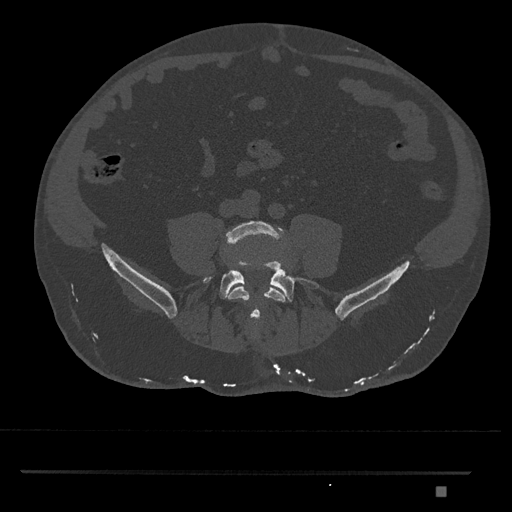
CT including the spine, one axial slice; slice 580 of 1134 in the series (ordered by position); 120 kVp; bone window (W 1800 / L 400 HU); 512 × 512 image matrix, field of view 429 × 429 mm. Patient: male, 65 years. Case-level facts recorded for this patient, not image findings: primary cancer: prostate.
Annotated regions visible in this slice (semi-automatically segmented with operator editing):
- L4 vertebra: box from (x=224, y=221) to (x=286, y=325) px
- L5 vertebra: (x=203, y=261)–(x=321, y=319)